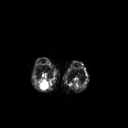
FDG PET of an extremity soft-tissue mass (from a PET/CT study), one axial slice; slice 164 of 267 in the series (ordered by position); 3.27 mm slice thickness; 128 × 128 image matrix, field of view 500 × 500 mm. Patient: female, 62 years. From the clinical record (not read from this slice): histological type: liposarcoma; site of the primary tumour: right thigh.
Outlined on this slice (expert contour drawn on MRI and transferred to this co-registered scan by the dataset authors):
- gross tumour volume (mass): bounding box [x1, y1, x2, y2] px = [39, 81, 49, 90]